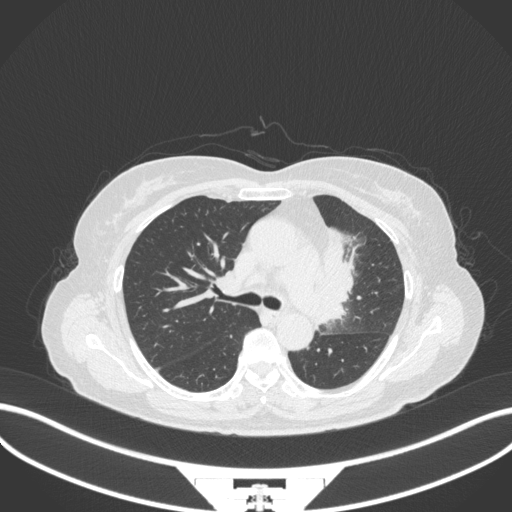
Chest CT, one axial slice; position 215 of 382 along the scan axis; reconstruction kernel B31f; lung window (W 1500 / L -600 HU); 1 mm slice thickness; 512 × 512 image matrix, field of view 400 × 400 mm. Female patient, age 64 years. Case-level facts recorded for this patient, not image findings: clinical TNM (as recorded): T2a N2 M0.
Structures marked on this image (rectangle marked by the reading radiologist):
- lung tumour (recorded histology: adenocarcinoma): box from (x=321, y=222) to (x=360, y=321) px